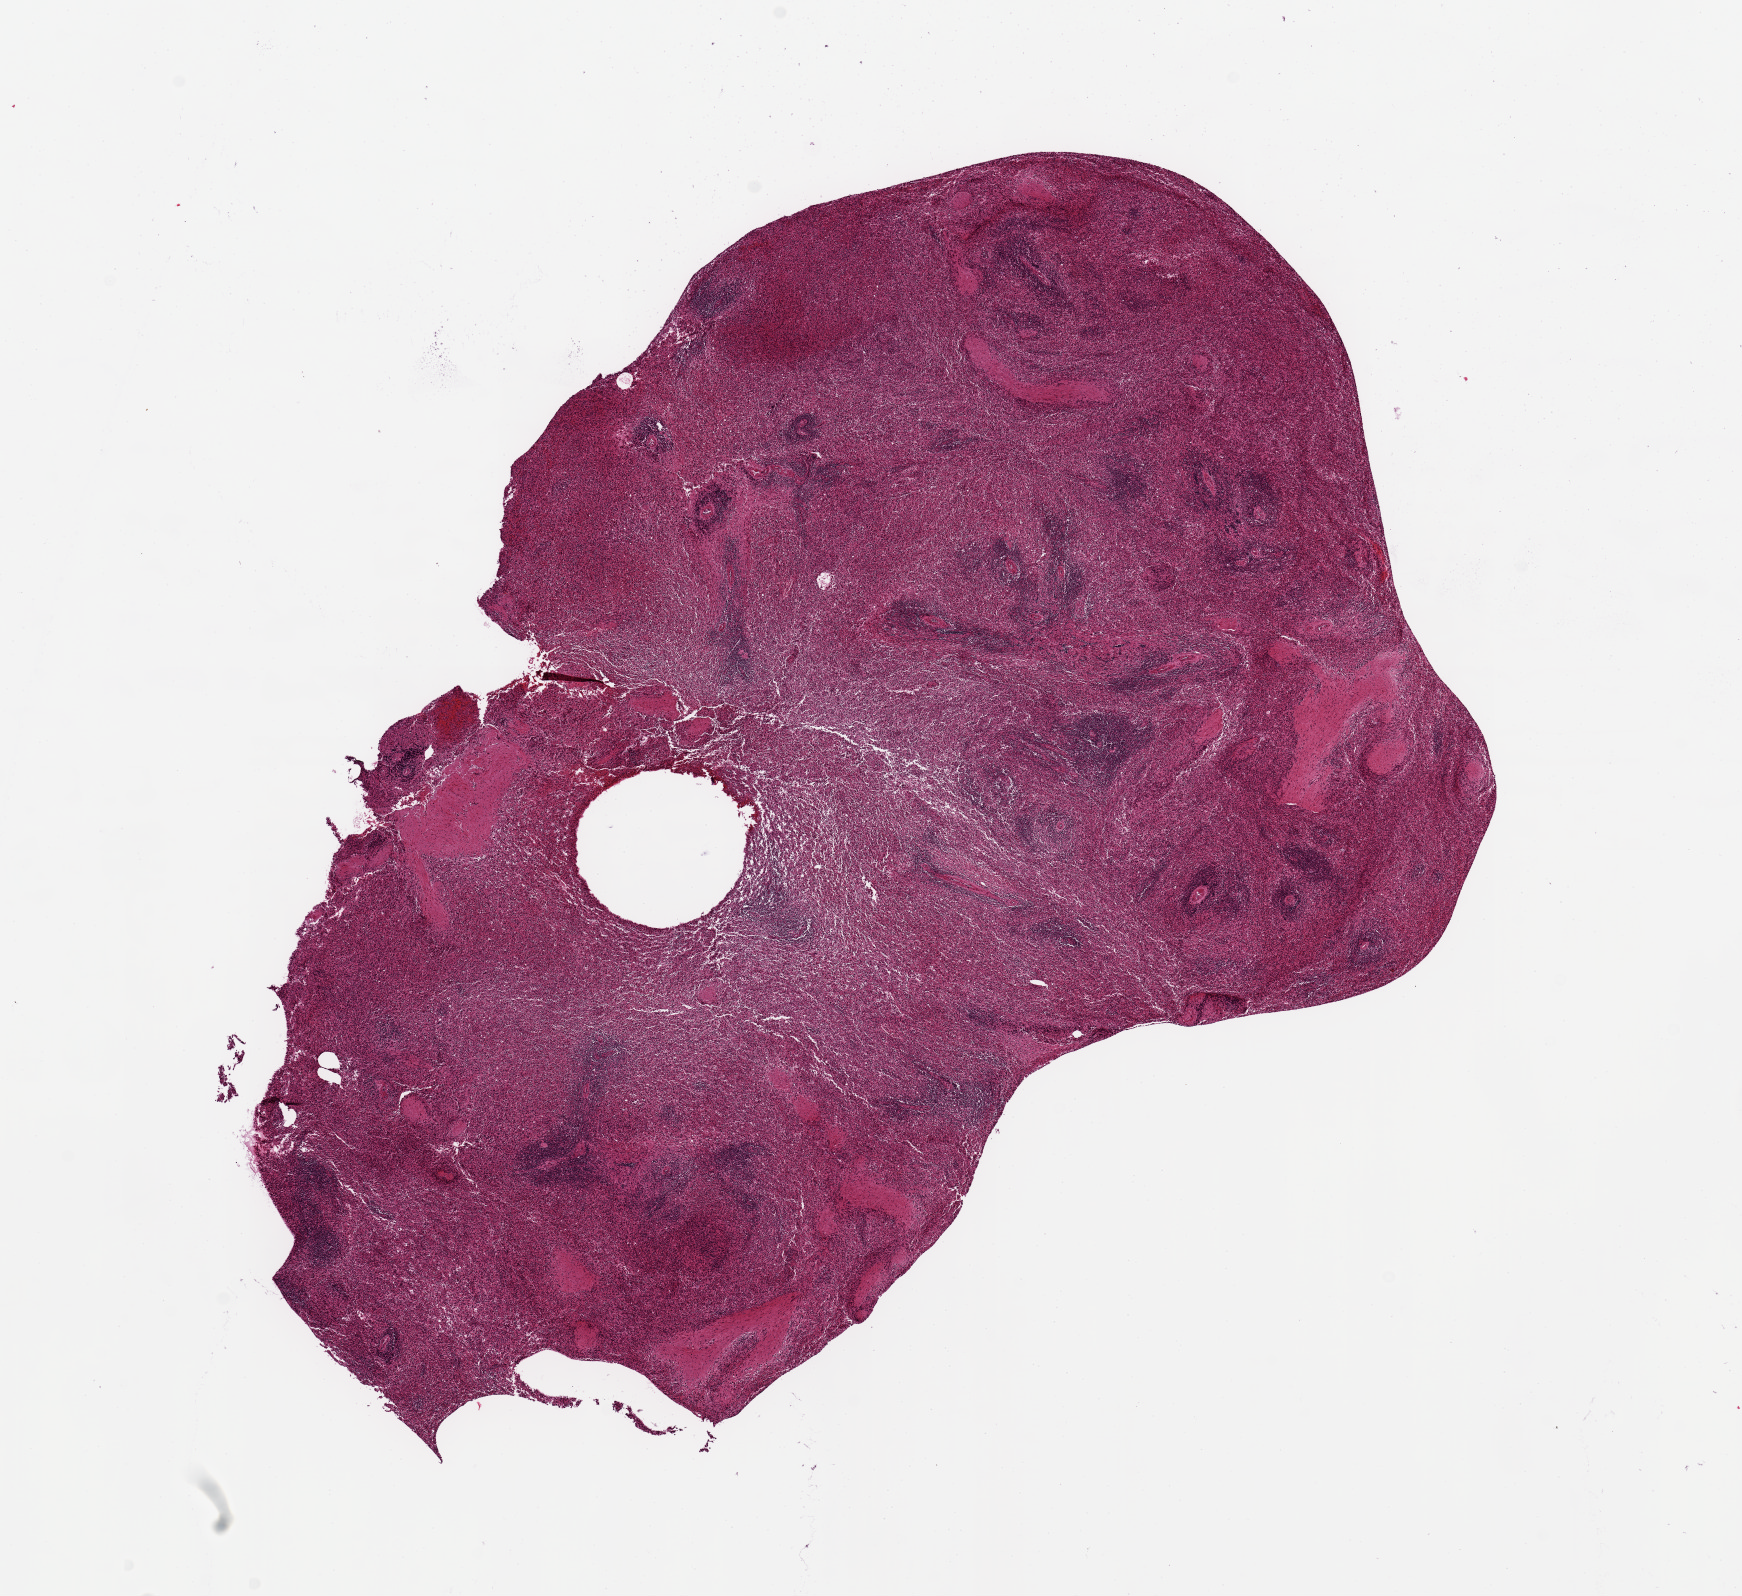
Hematoxylin and eosin (H&E) whole-slide image, brightfield — shown as a low-resolution overview of the whole scanned area (about 13.8 x 12.6 mm); PAXgene-fixed paraffin-embedded (PFPE) section; section of spleen (target tissue); donor tissue sample. Donor: male.
Review note (as recorded): 10x8mm. Central poor fixation.